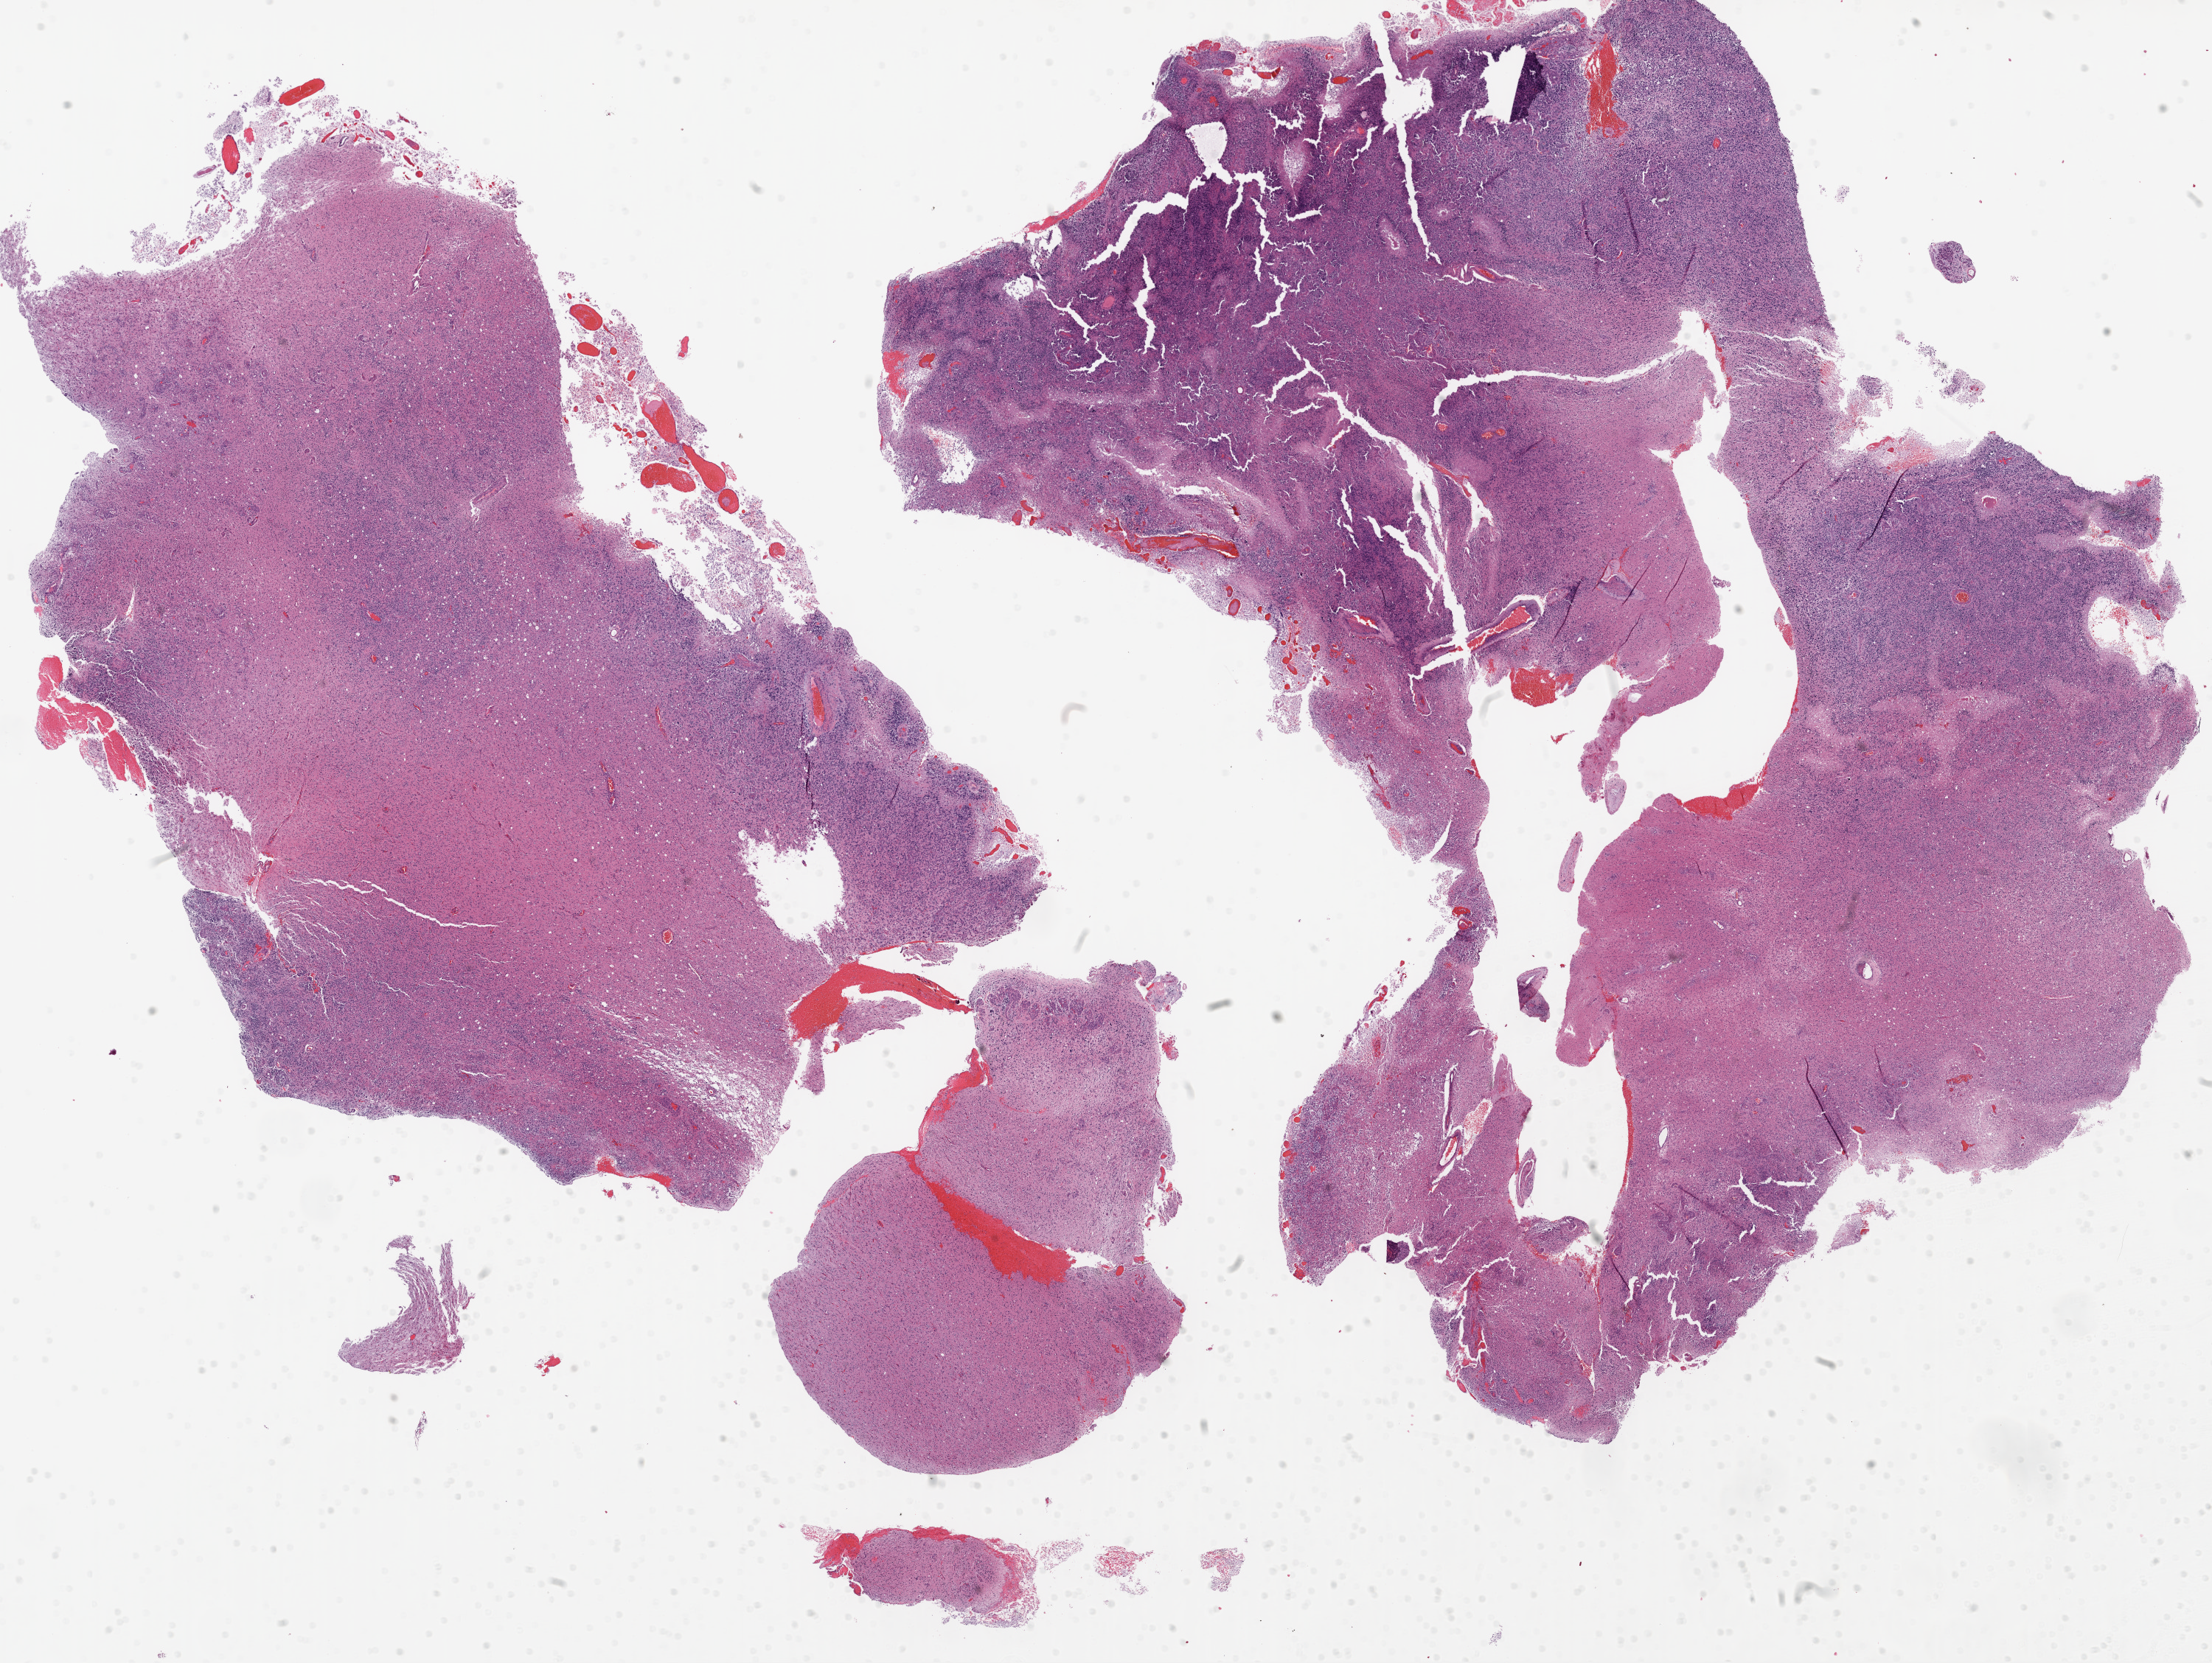
Digitized Hematoxylin and eosin (H&E) stained tissue section (whole slide) — shown as a low-resolution overview of the whole scanned area (about 24.1 x 18.1 mm); FFPE section; brain, primary tumour sample. Male patient; age at initial diagnosis 70 years.
* pathologic diagnosis: Glioblastoma